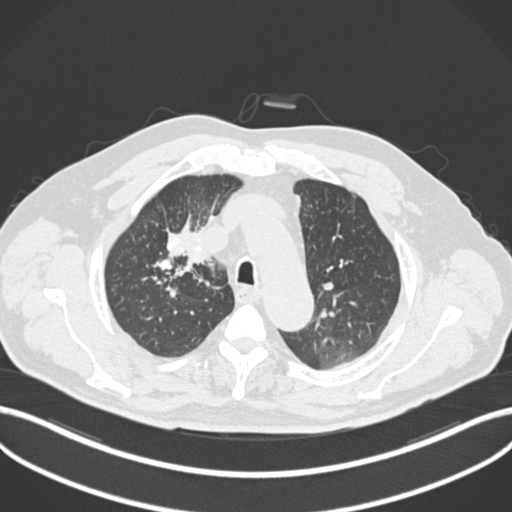
Chest CT, one axial slice. Slice 154 of 255 in the series (ordered by position). Reconstruction kernel B30f. 120 kVp. Lung window (W 1500 / L -600 HU). 1 mm slice thickness. 512 × 512 image matrix, field of view 400 × 400 mm. Male patient, age 60 years. Case-level facts recorded for this patient, not image findings: clinical TNM (as recorded): T1b N1 M0.
Annotated regions visible in this slice (bounding box drawn by a radiologist):
- lung tumour (recorded histology: squamous cell carcinoma): bounding box <159,220,217,270> (left, top, right, bottom; pixels)